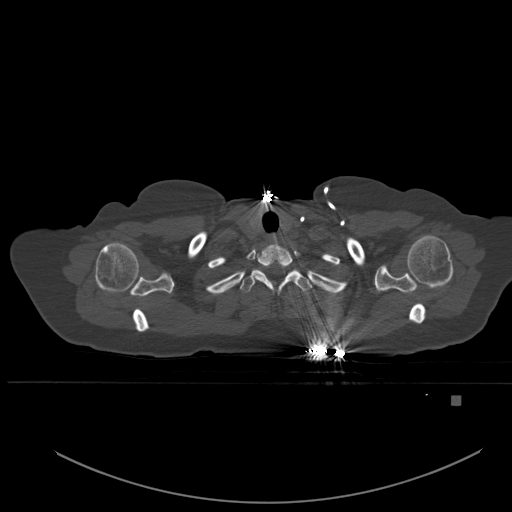
CT including the spine, one axial slice. Position 424 of 651 along the scan axis. Bone window (W 1800 / L 400 HU). 1.5 mm slice thickness. 512 × 512 image matrix, field of view 443 × 443 mm. Female patient, age 49 years. From the clinical record (not read from this slice): primary cancer: breast; vertebrae with lytic lesions (as recorded): L3, T12, L4.
Outlined on this slice (semi-automatically segmented with operator editing):
- T1 vertebra: bounding box [x1, y1, x2, y2] px = [240, 270, 313, 294]